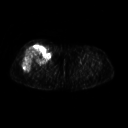
FDG PET of an extremity soft-tissue mass (from a PET/CT study), one axial slice. Position 249 of 311 along the scan axis. 3.27 mm slice thickness. 128 × 128 image matrix, field of view 500 × 500 mm. Female patient, age 57 years. Case-level facts recorded for this patient, not image findings: histological type: pleiomorphic undifferentiated sarcoma; grade: high; site of the primary tumour: right quadricep.
Annotated regions visible in this slice (expert contour drawn on MRI and transferred to this co-registered scan by the dataset authors):
- tumour plus oedema (research contour): bounding box (x1, y1, x2, y2) in pixels: (23, 46, 50, 72)
- tumour (research contour): (23, 46, 50, 72)